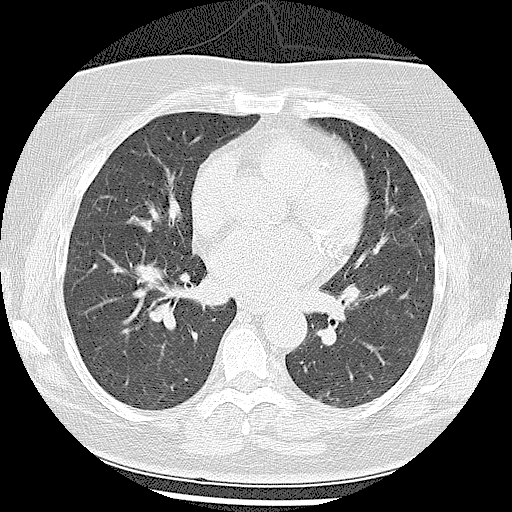
Low-dose screening chest CT, one axial slice. Position 47 of 102 along the scan axis. Lung window (W 1500 / L -600 HU). 2.5 mm slice thickness. 512 × 512 image matrix, field of view 350 × 350 mm.
Outlined on this slice (expert manual segmentation):
- lesion 1 (tumor, middle lobe of right lung): bounding box [x1, y1, x2, y2] px = [128, 215, 153, 233]